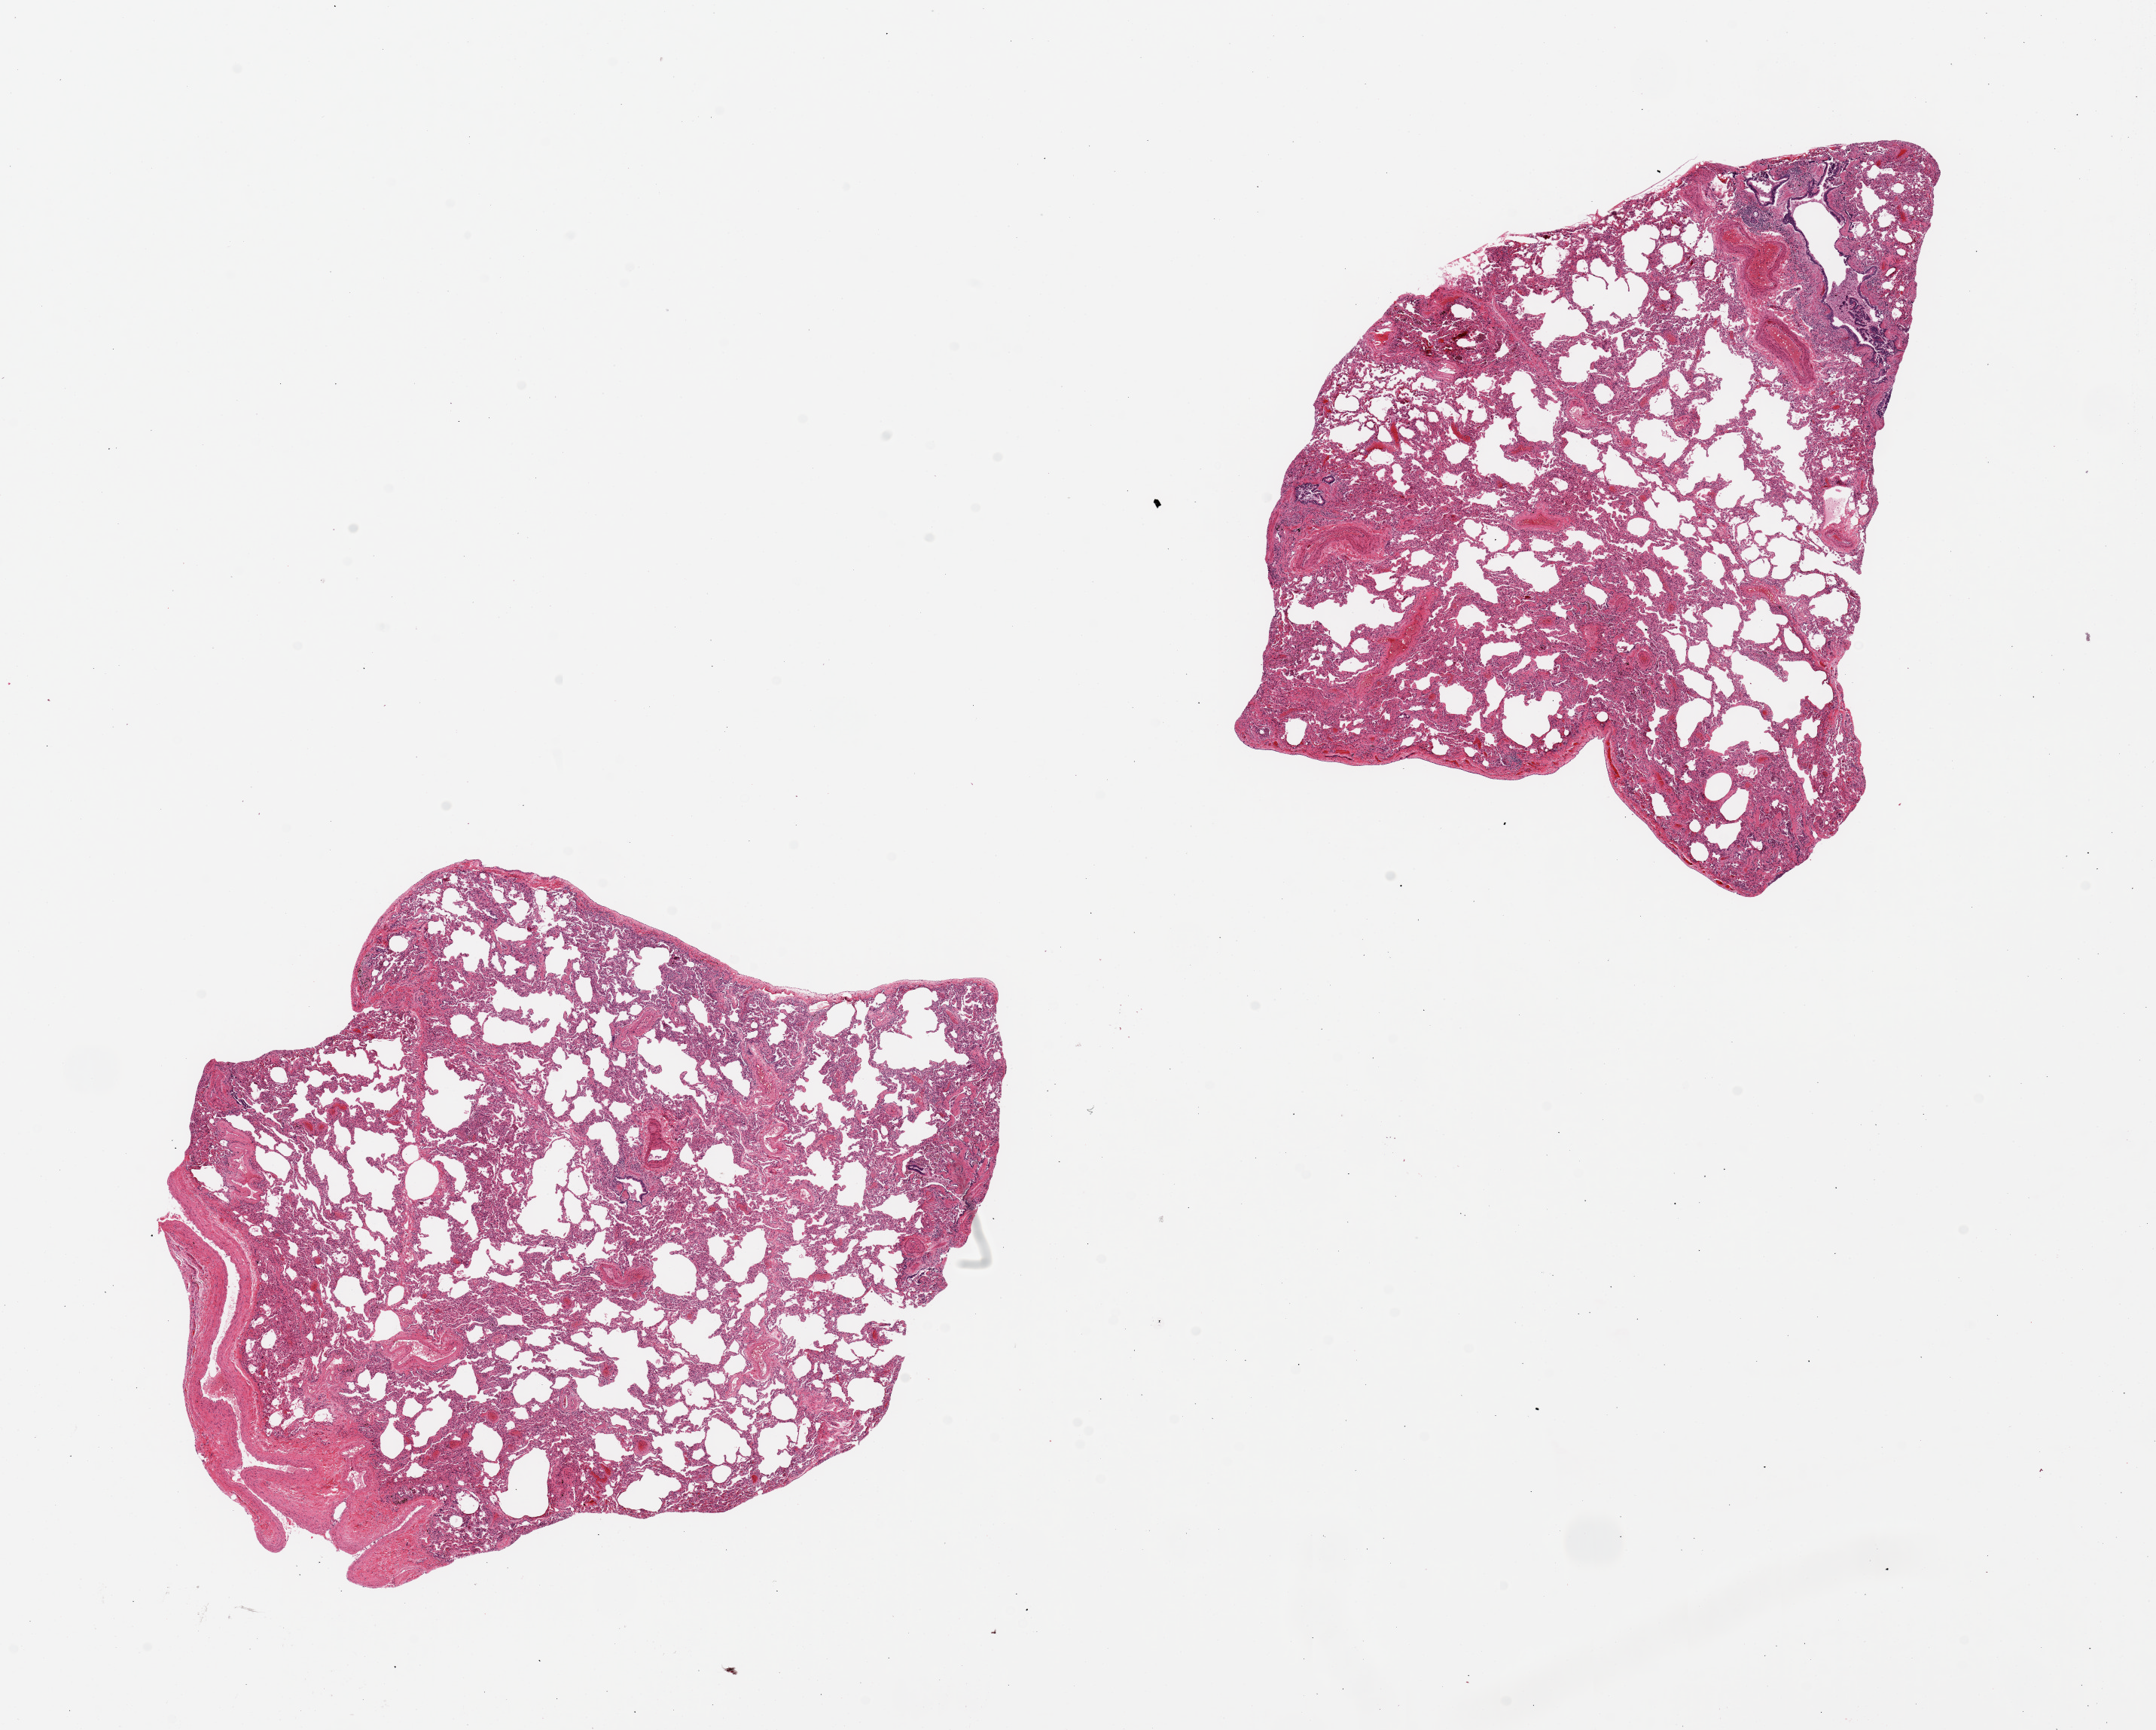
Hematoxylin and eosin (H&E) whole-slide image, whole scanned area (about 22.6 x 18.2 mm) shown as a low-resolution overview. PAXgene-fixed, paraffin-embedded tissue. Target tissue: lung. Tissue donor sample.
* pathologist's review note for this sample: 2 pieces ~8x7mm, emphysemaous changes, congestion, badly autolyzed, vascular structures